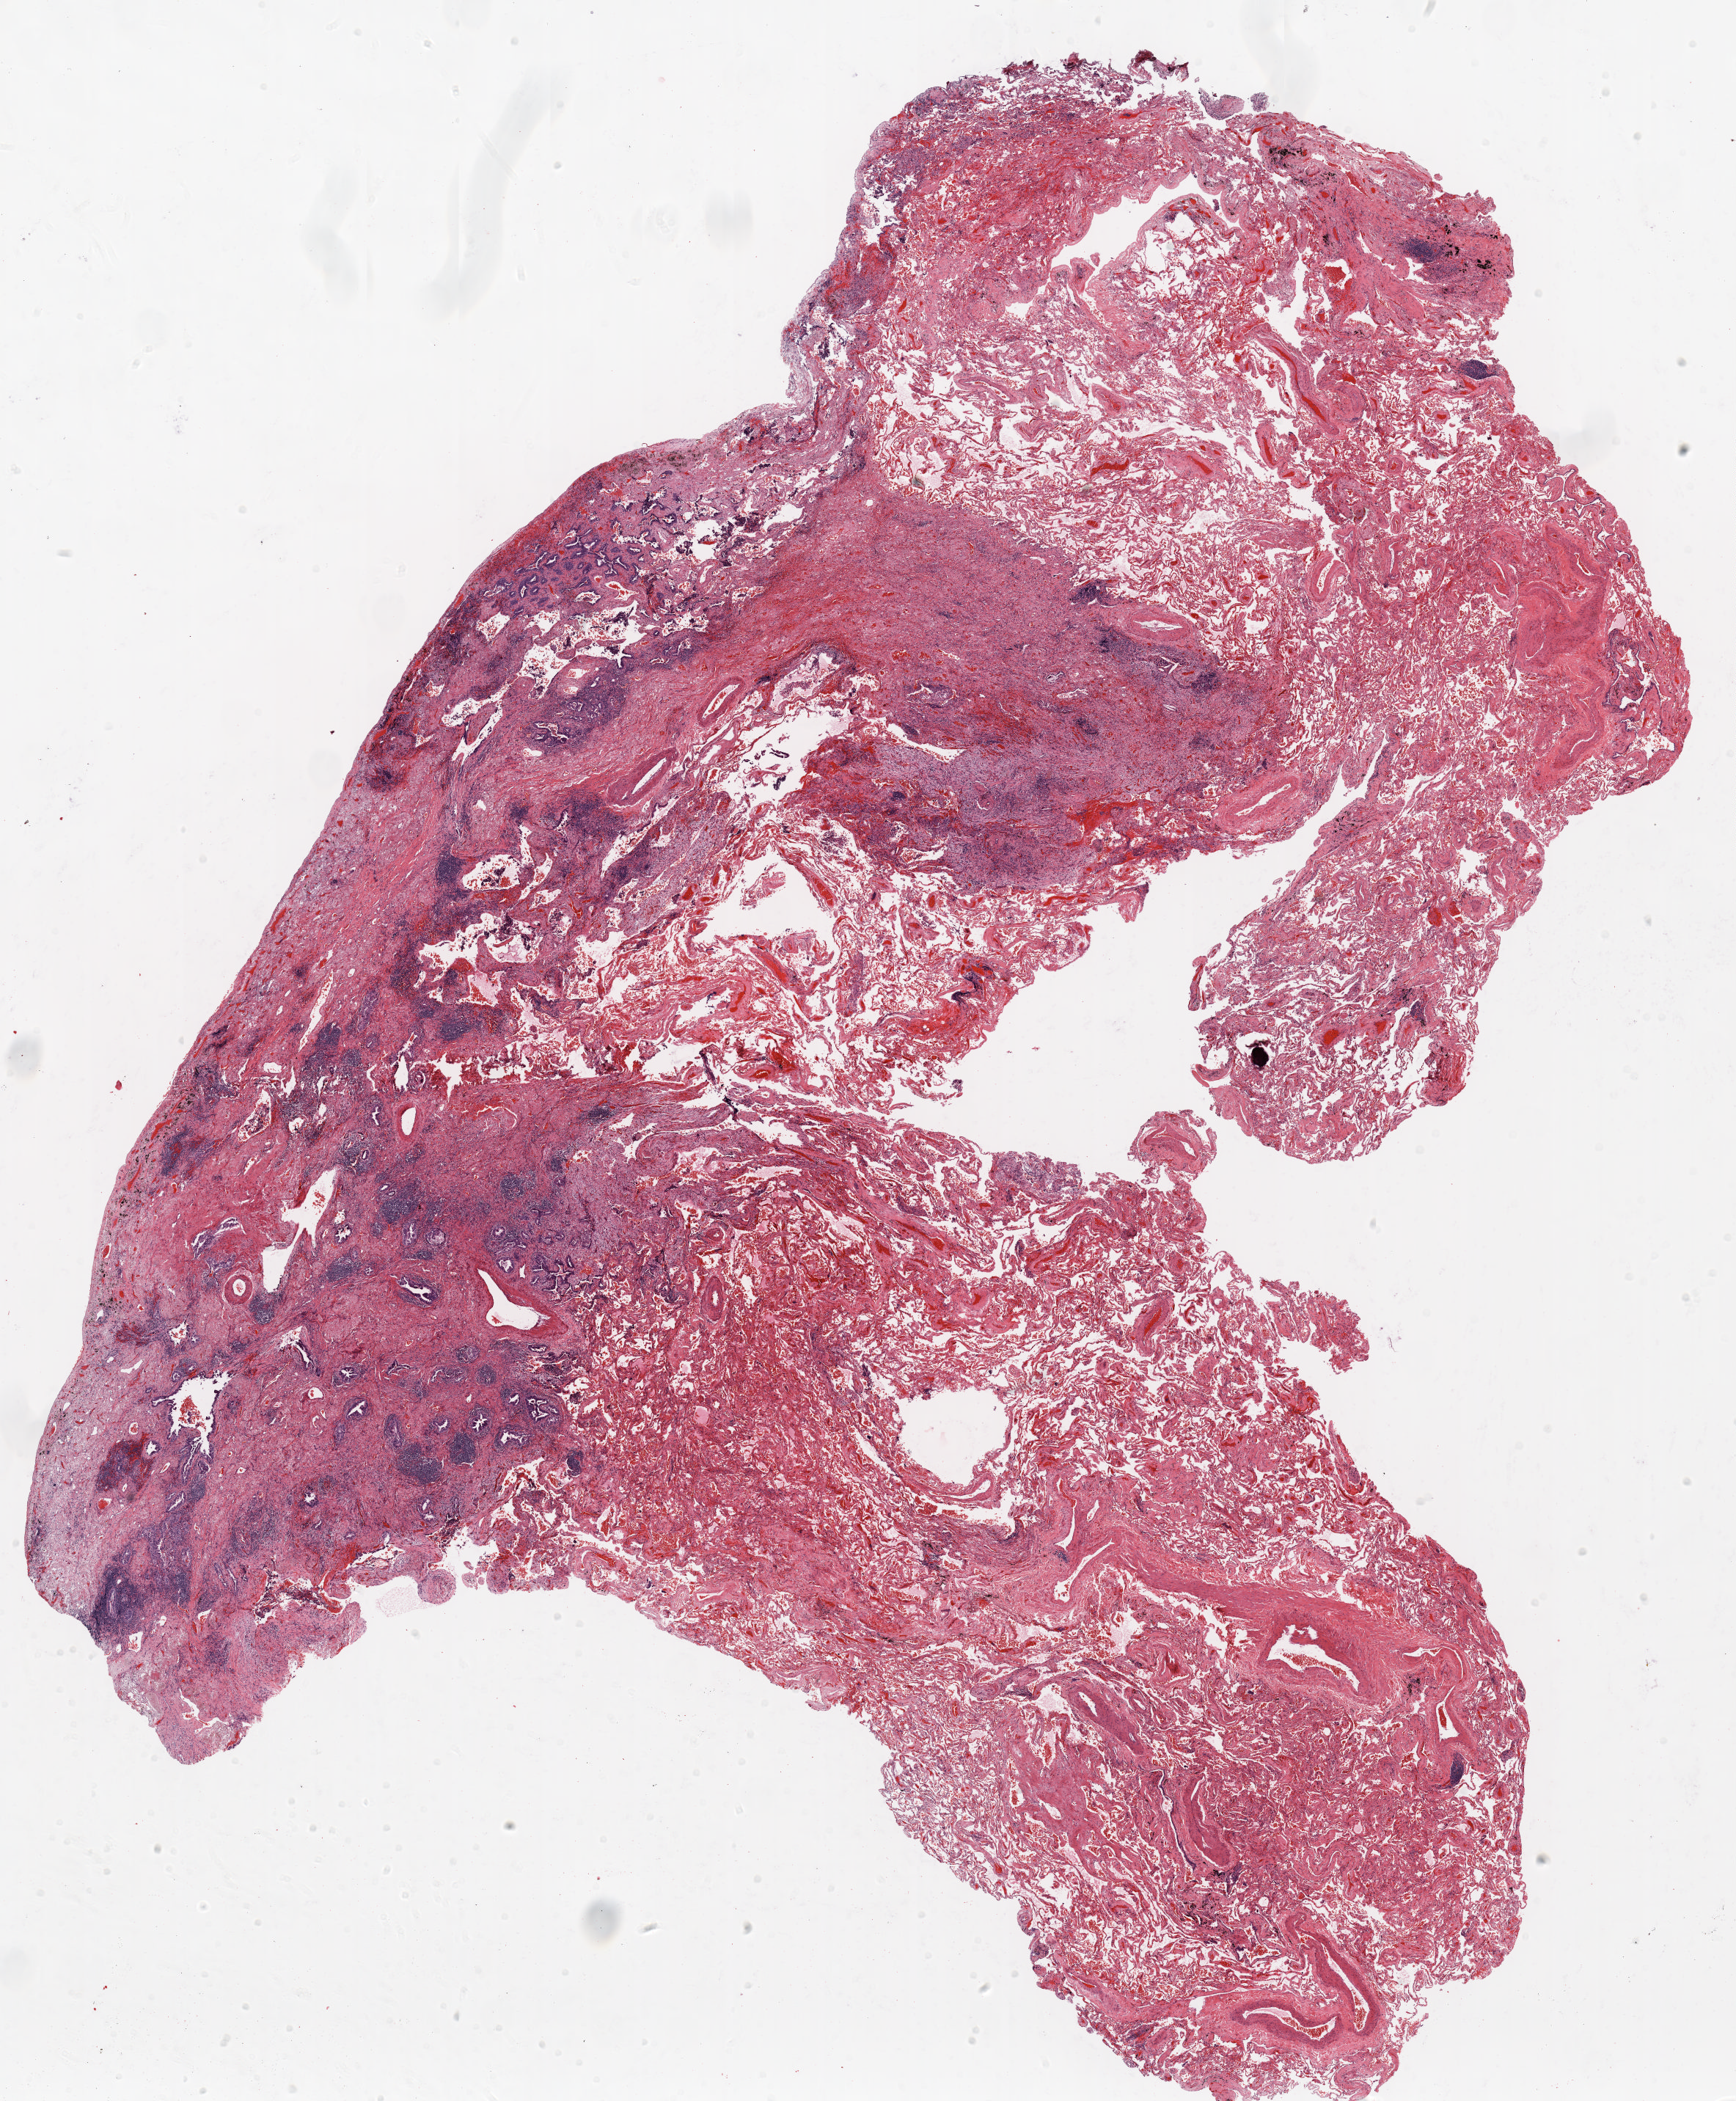
Whole-slide histology image, Hematoxylin and eosin (H&E) stained — shown as a low-resolution overview of the whole scanned area (about 19.0 x 23.0 mm, acquisition: 20x scan); formalin-fixed paraffin-embedded (FFPE) section; lung. Male patient, aged 73 at enrolment. Grade: poorly differentiated (G3).
* stage (AJCC 6th edition): IA
* ICD-O-3 topography: upper lobe of lung (C34.1)
* tumour size (pathology): 30 mm
* primary tumour location (clinical record): right upper lobe
* participant's lung-cancer diagnosis: Adenocarcinoma, NOS (ICD-O-3 8140/3)